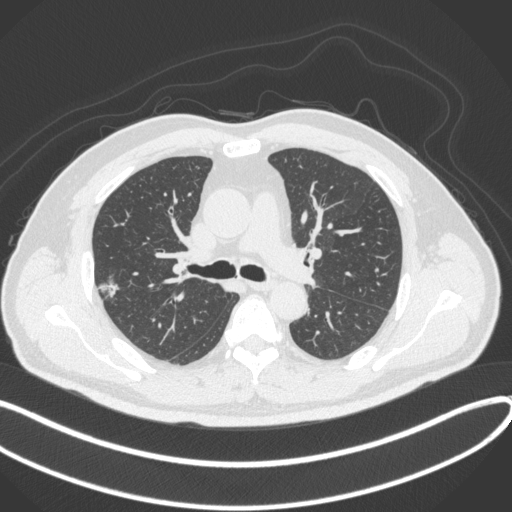
Chest CT, one axial slice. Position 217 of 373 along the scan axis. Lung window (W 1500 / L -600 HU). 1 mm slice thickness. 512 × 512 image matrix. Male patient, age 60 years. Case-level facts recorded for this patient, not image findings: clinical TNM (as recorded): T1c N0 M0.
Annotated regions visible in this slice (rectangle marked by the reading radiologist):
- lung tumour (recorded histology: adenocarcinoma): bounding box [x1, y1, x2, y2] px = [94, 273, 126, 307]